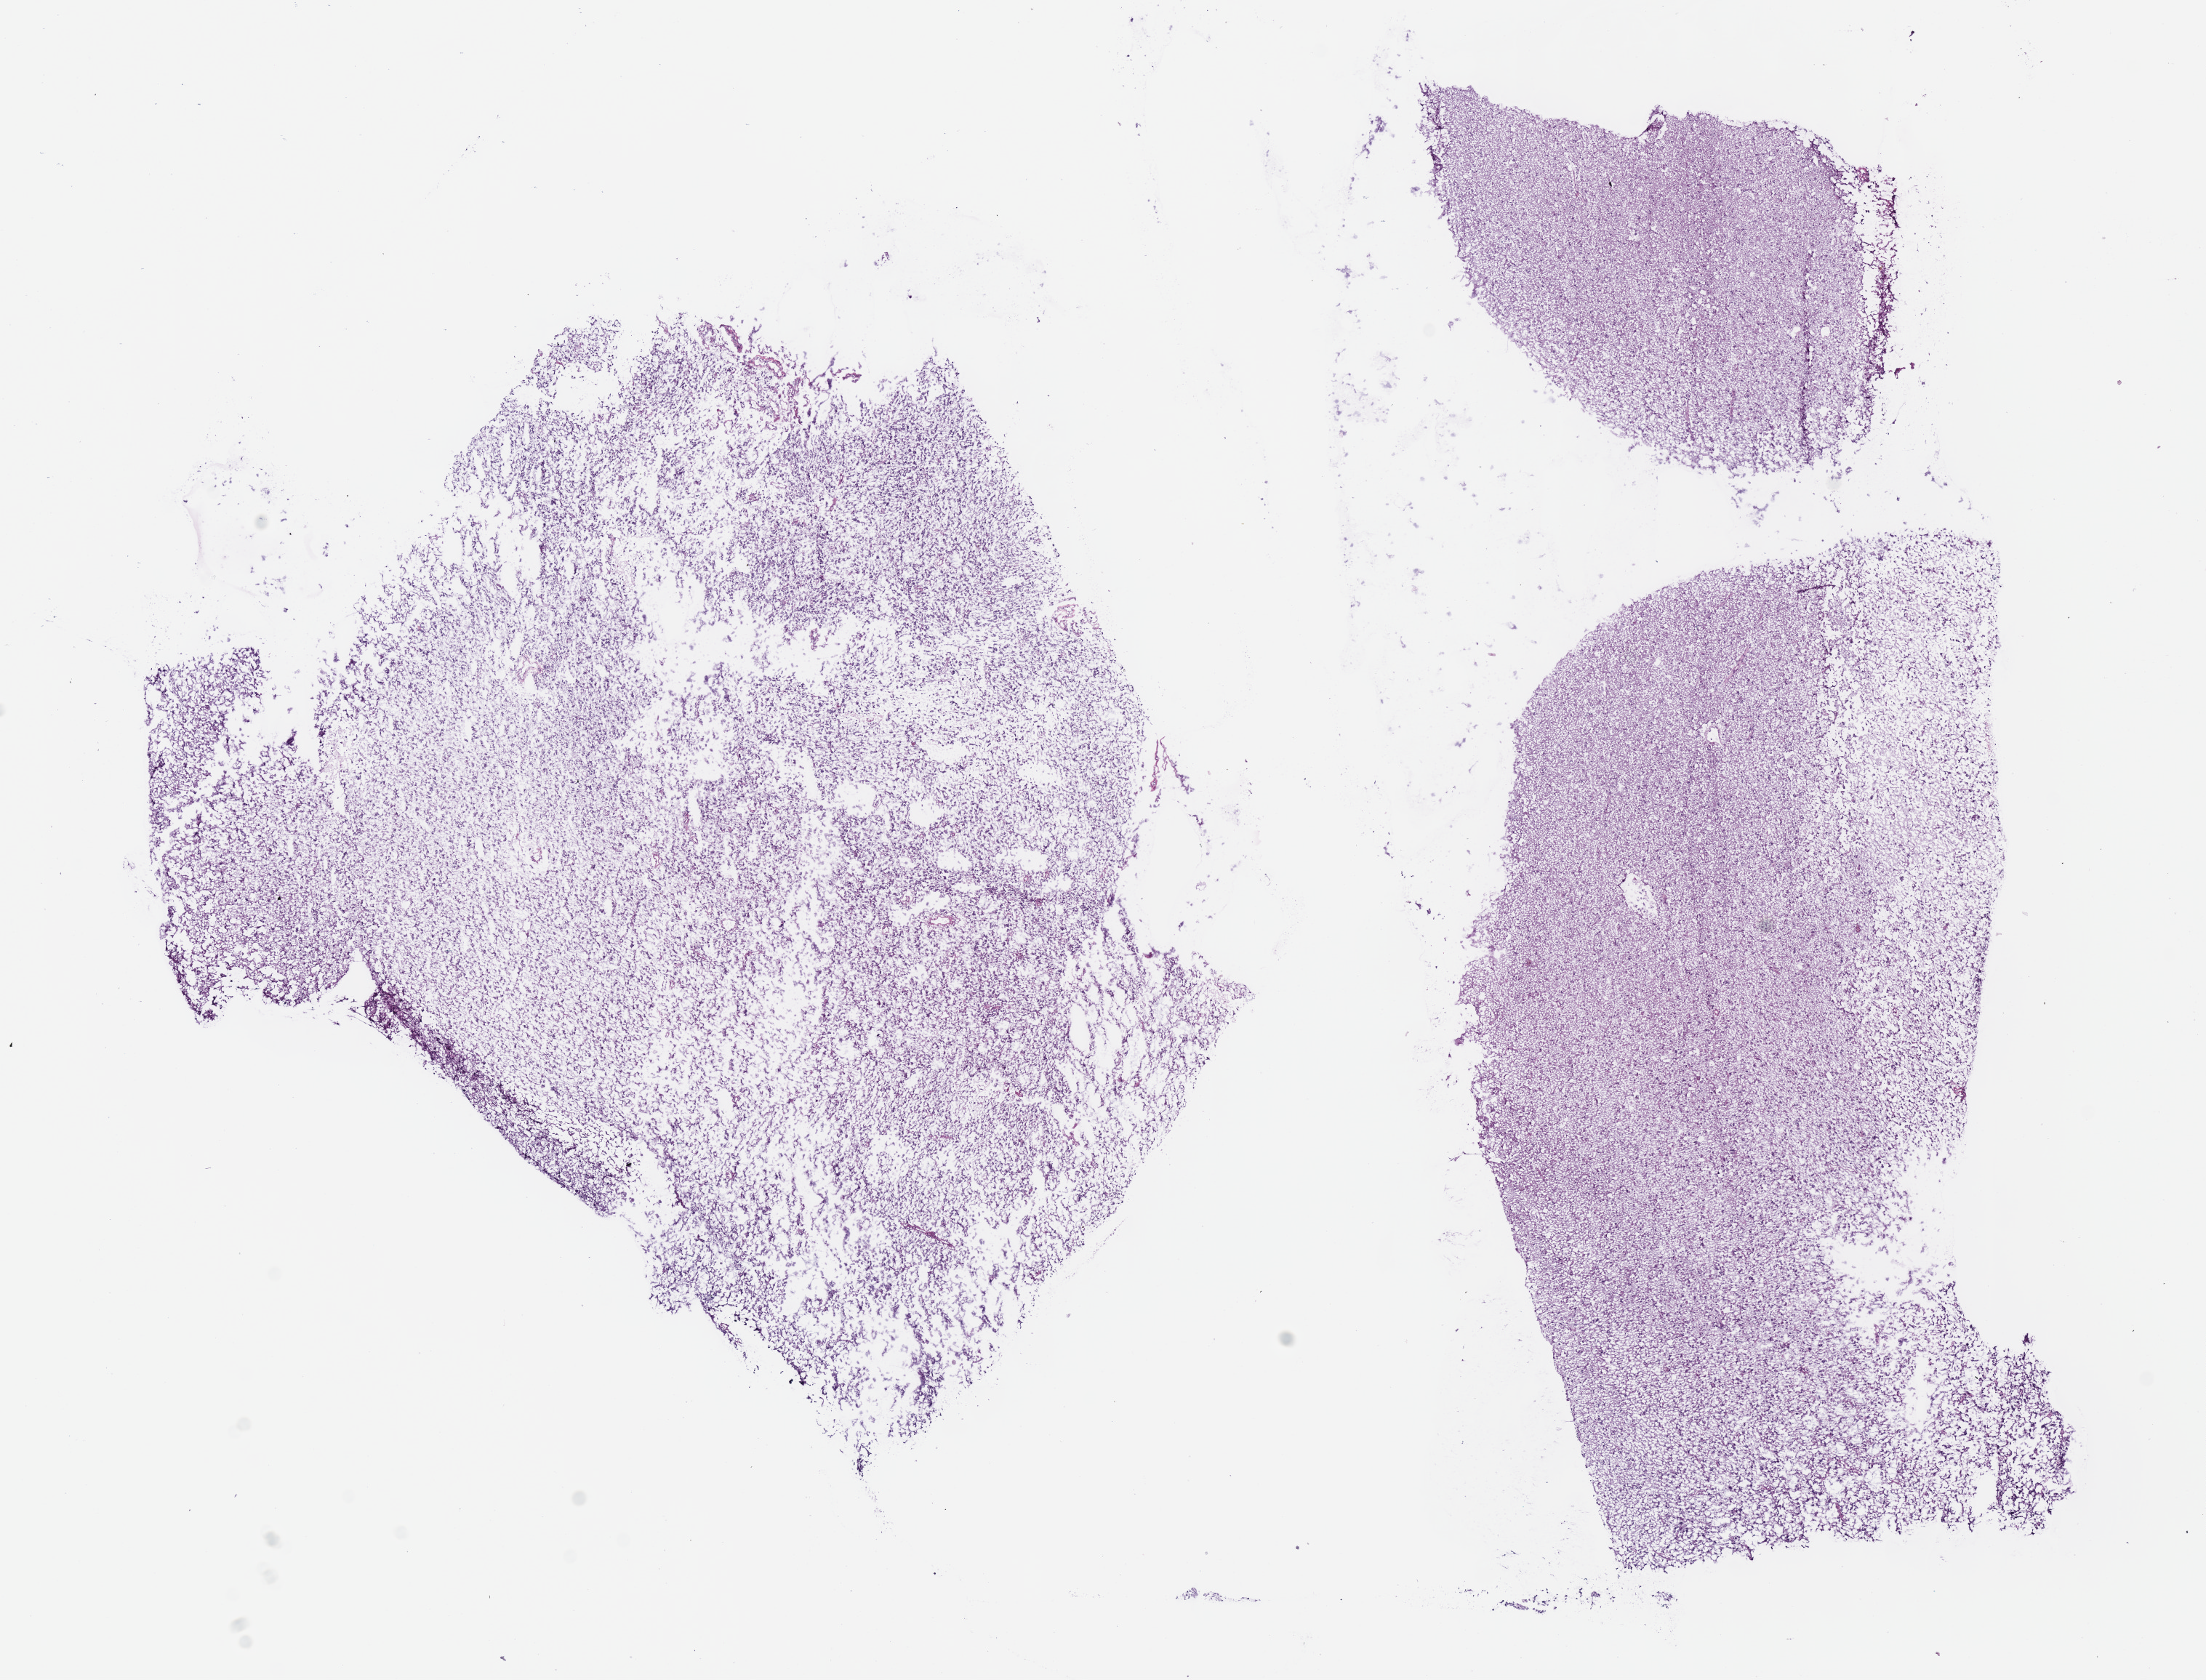
Digitized H&E tissue section (whole slide) — shown as a low-resolution overview of the whole scanned area (about 12.0 x 9.1 mm). Frozen section from the bottom of the tissue portion. Sample: primary tumour, brain. Male patient; age at initial diagnosis 26 years. Histologic grade: G2 (moderately differentiated). Slide review estimates, as recorded: tumour cells 100%, tumour nuclei 70%, normal cells 0%, stromal cells 0%, necrosis 0%.
• diagnosis: Astrocytoma, NOS (cerebrum)